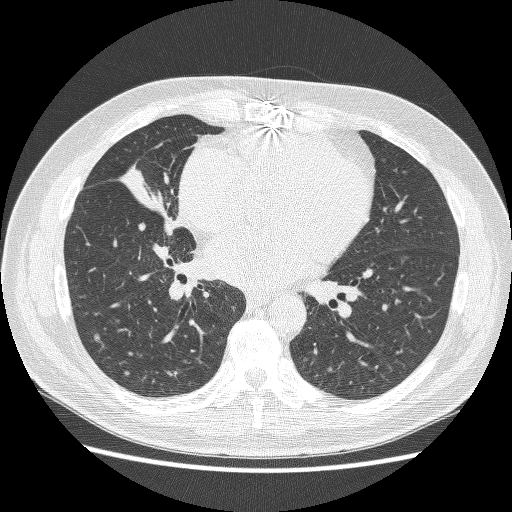
Low-dose screening chest CT, axial slice; baseline screening round; lung window (W 1500 / L -600 HU); 1.25 mm slice thickness; lung (sharp) reconstruction kernel (BONE); slice 122 of 251 in the series. Male participant, aged 59 years at enrolment. Former smoker at enrolment.
Lesion marked by an expert reader, box from (x=109, y=156) to (x=195, y=244) px. Screening reader's record for this exam: no non-calcified nodule ≥4 mm recorded. Official screen result: positive, change unspecified: nodule(s) >= 4 mm or enlarging nodule(s), mass(es), or other non-specific abnormalities suspicious for lung cancer. Later outcome: lung cancer diagnosed 24 days after this screen — adenocarcinoma, NOS, right middle lobe, poorly differentiated (G3), stage IV (AJCC 6th edition), 54 mm at pathology.